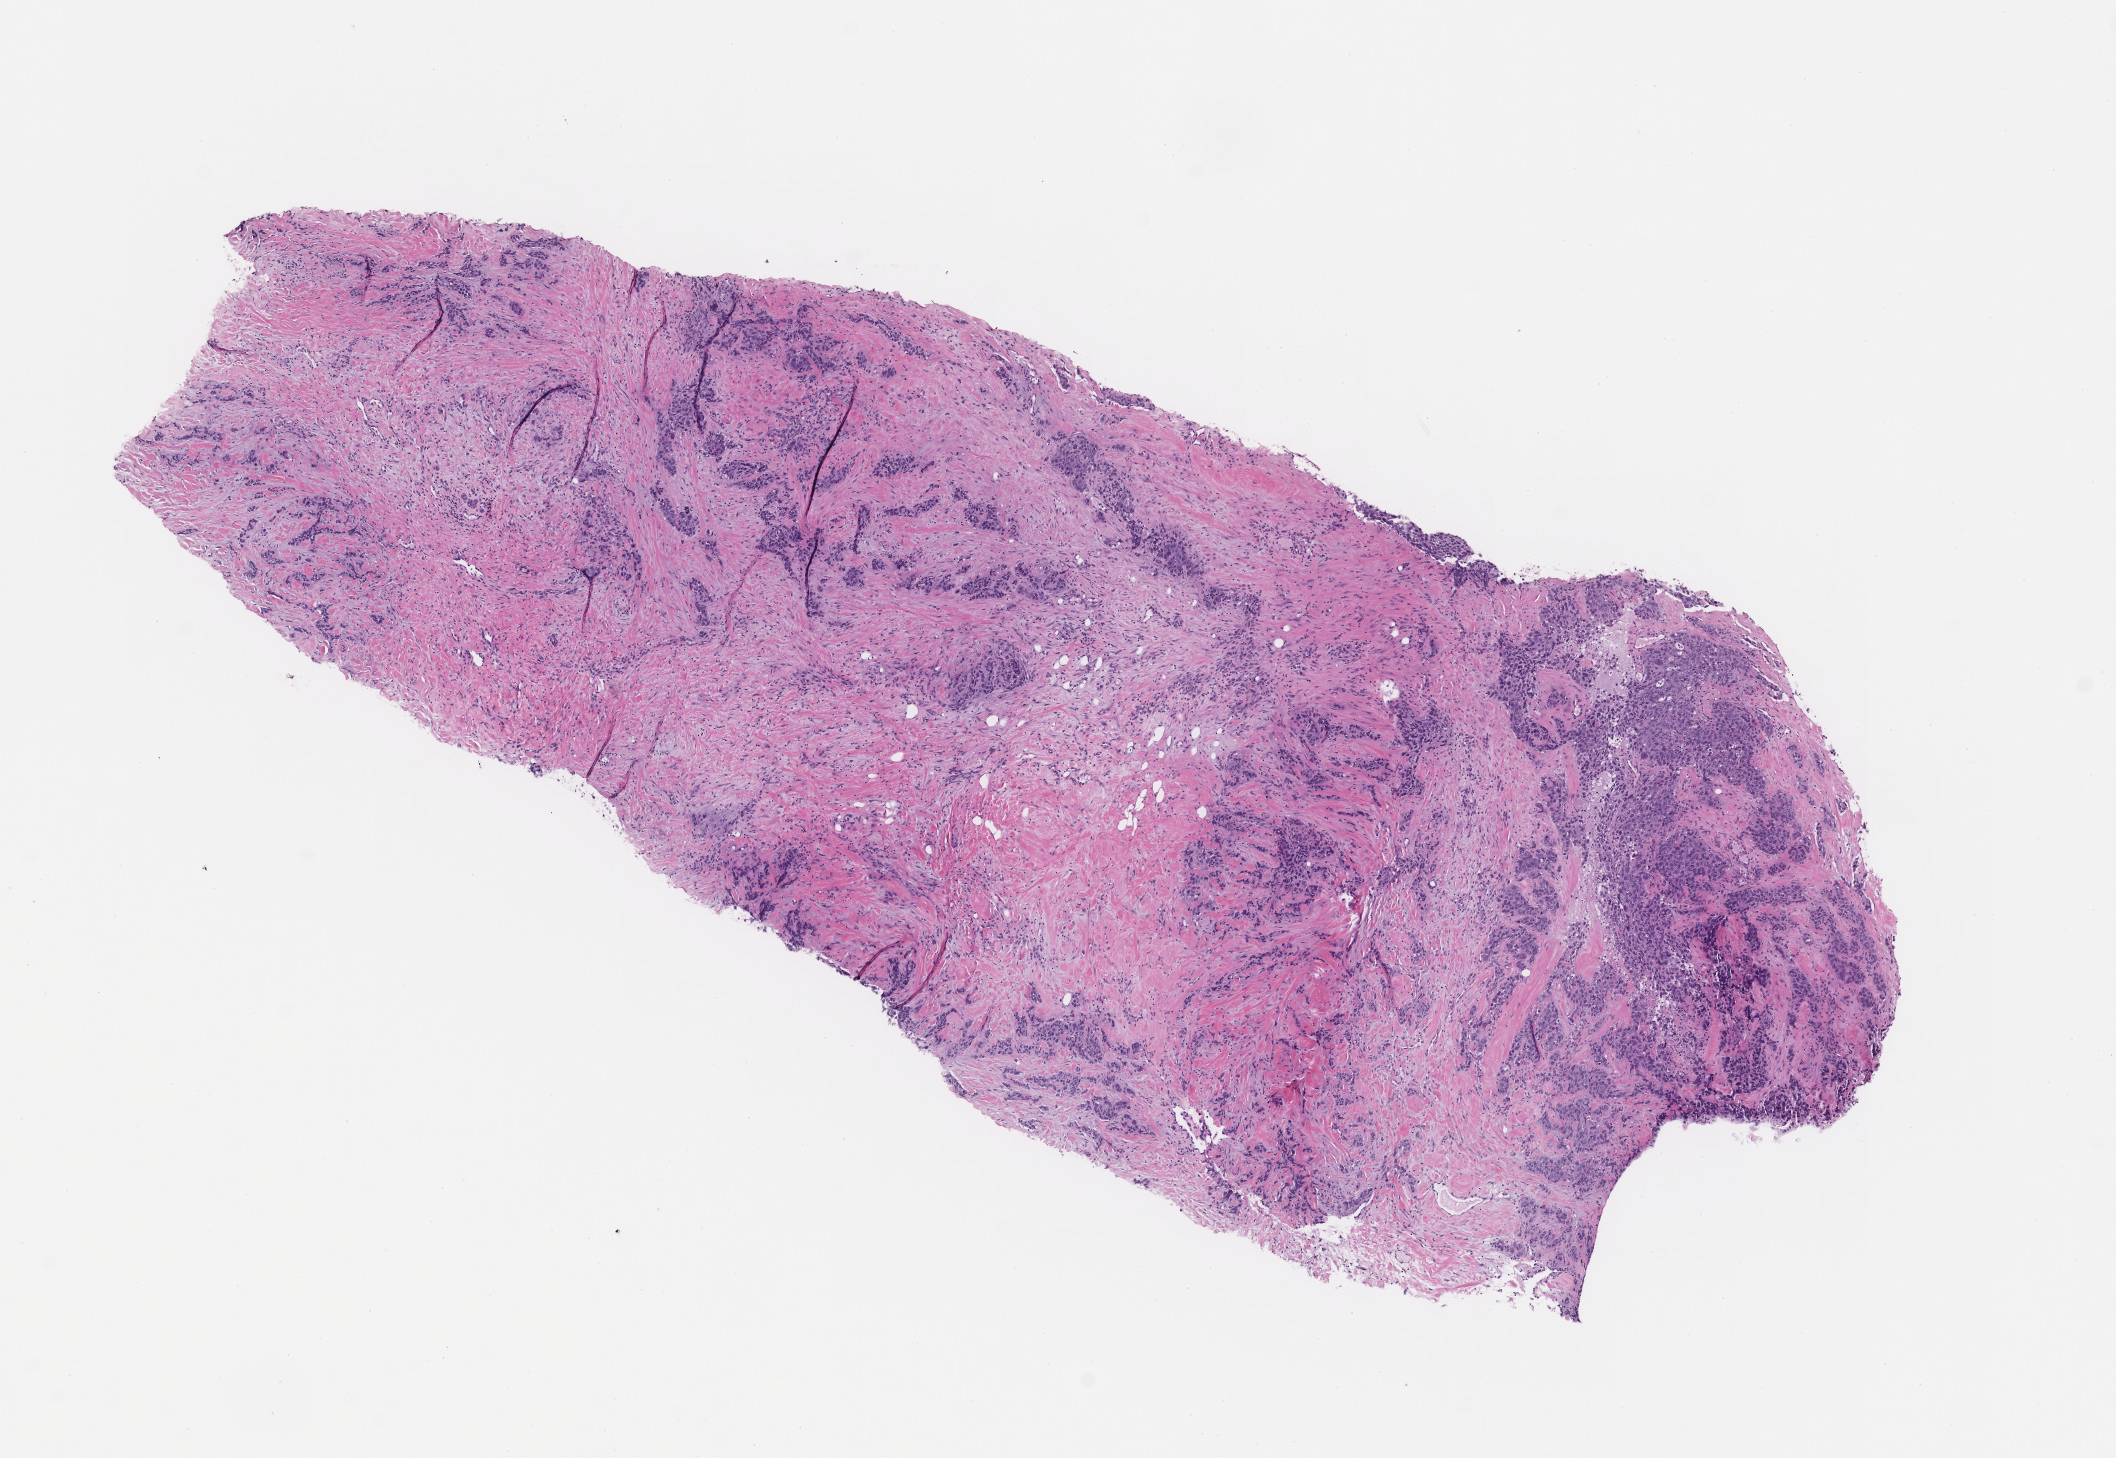
Digitized haematoxylin and eosin-stained section, a low-resolution overview of the entire scanned area, about 8.5 x 5.9 mm. Formalin-fixed paraffin-embedded section. Tissue site: breast. Specimen time point: collected at baseline (before treatment). Female patient.
This section: primary tumor. Diagnosis: Invasive Breast Carcinoma.